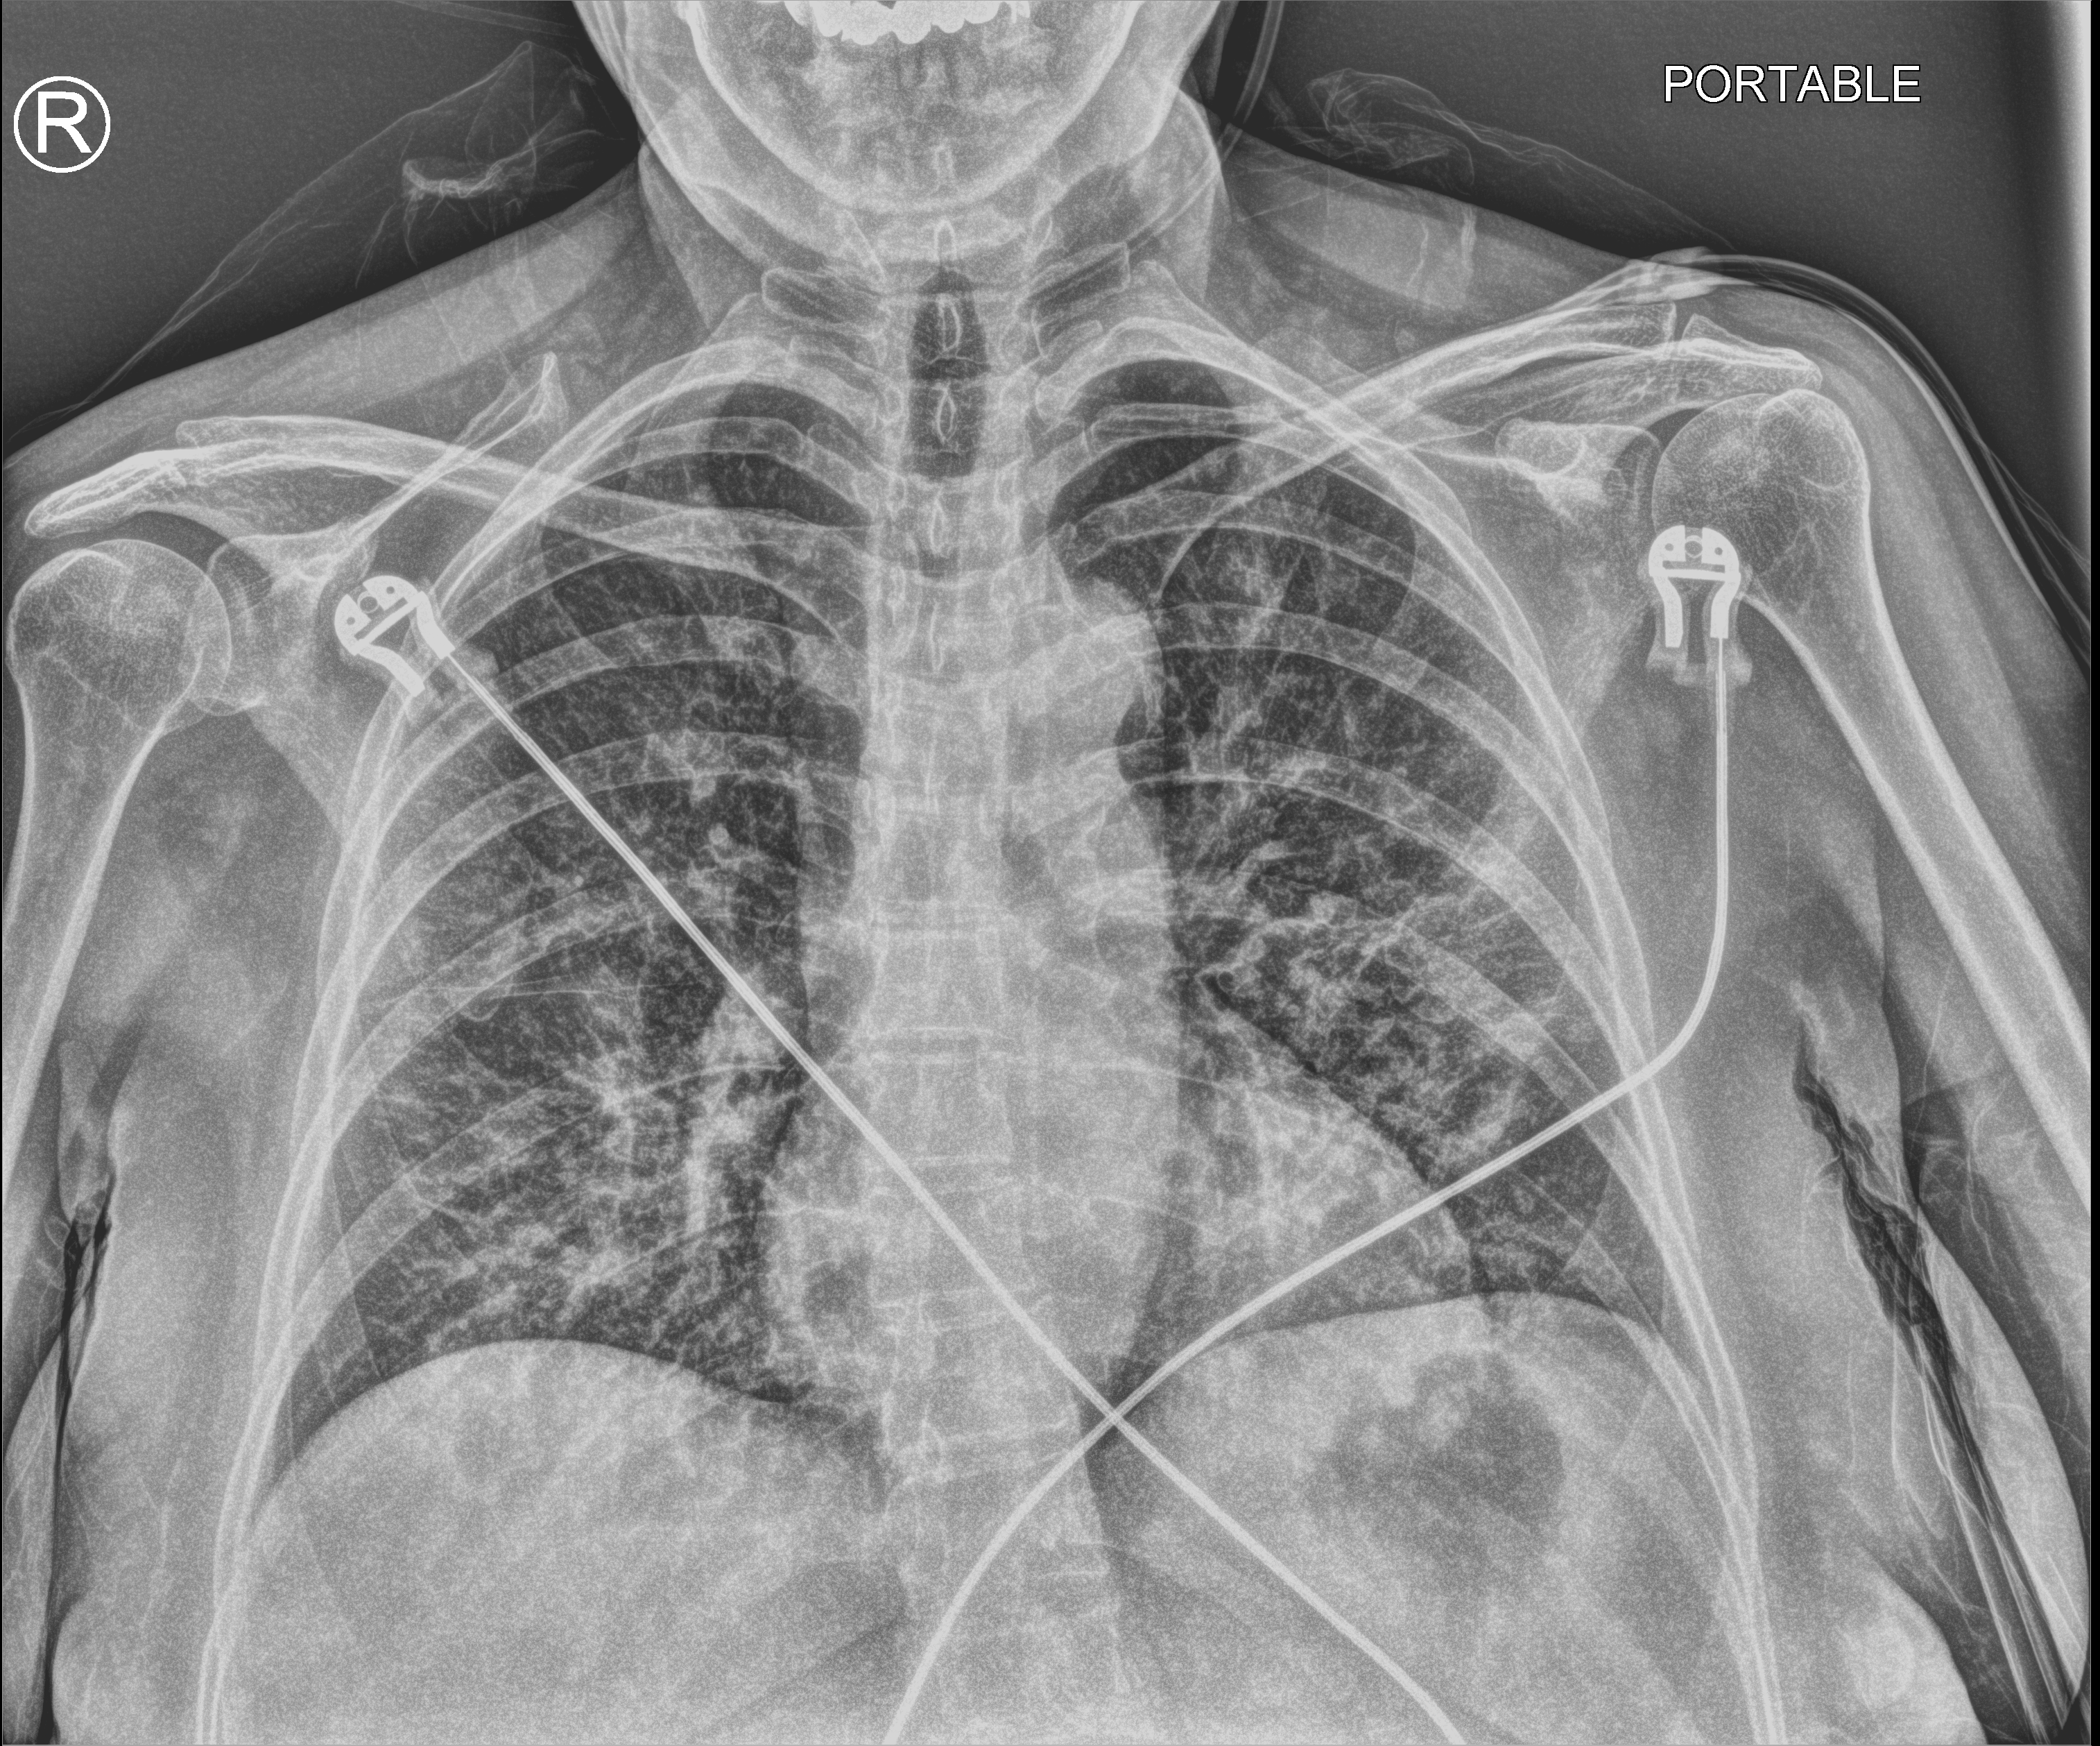
Bedside chest radiograph (computed radiography), anteroposterior (AP) projection. Patient hospitalised with COVID-19; female, aged 18–59 years.
Admission-level facts for this patient (not findings on this image; timing relative to this image not recorded): admitted to intensive care during this hospital stay: no; mechanically ventilated during this hospital stay: no.